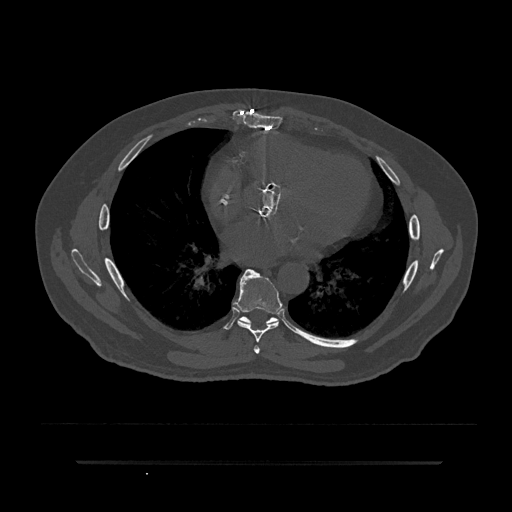
CT including the spine, one axial slice. Slice 463 of 797 in the series (ordered by position). Reconstruction kernel Br40s/3. Bone window (W 1800 / L 400 HU). 0.5 mm slice thickness. 512 × 512 image matrix, field of view 464 × 464 mm. Male patient, age 59 years. From the clinical record (not read from this slice): primary cancer: bile ducts; vertebrae with lytic lesions (as recorded): T10.
Structures marked on this image (semi-automatic segmentation, software-assisted and operator-edited):
- T6 vertebra: bounding box [x1, y1, x2, y2] px = [254, 345, 260, 354]
- T7 vertebra: [233, 269, 282, 343]
- T8 vertebra: [238, 311, 296, 333]